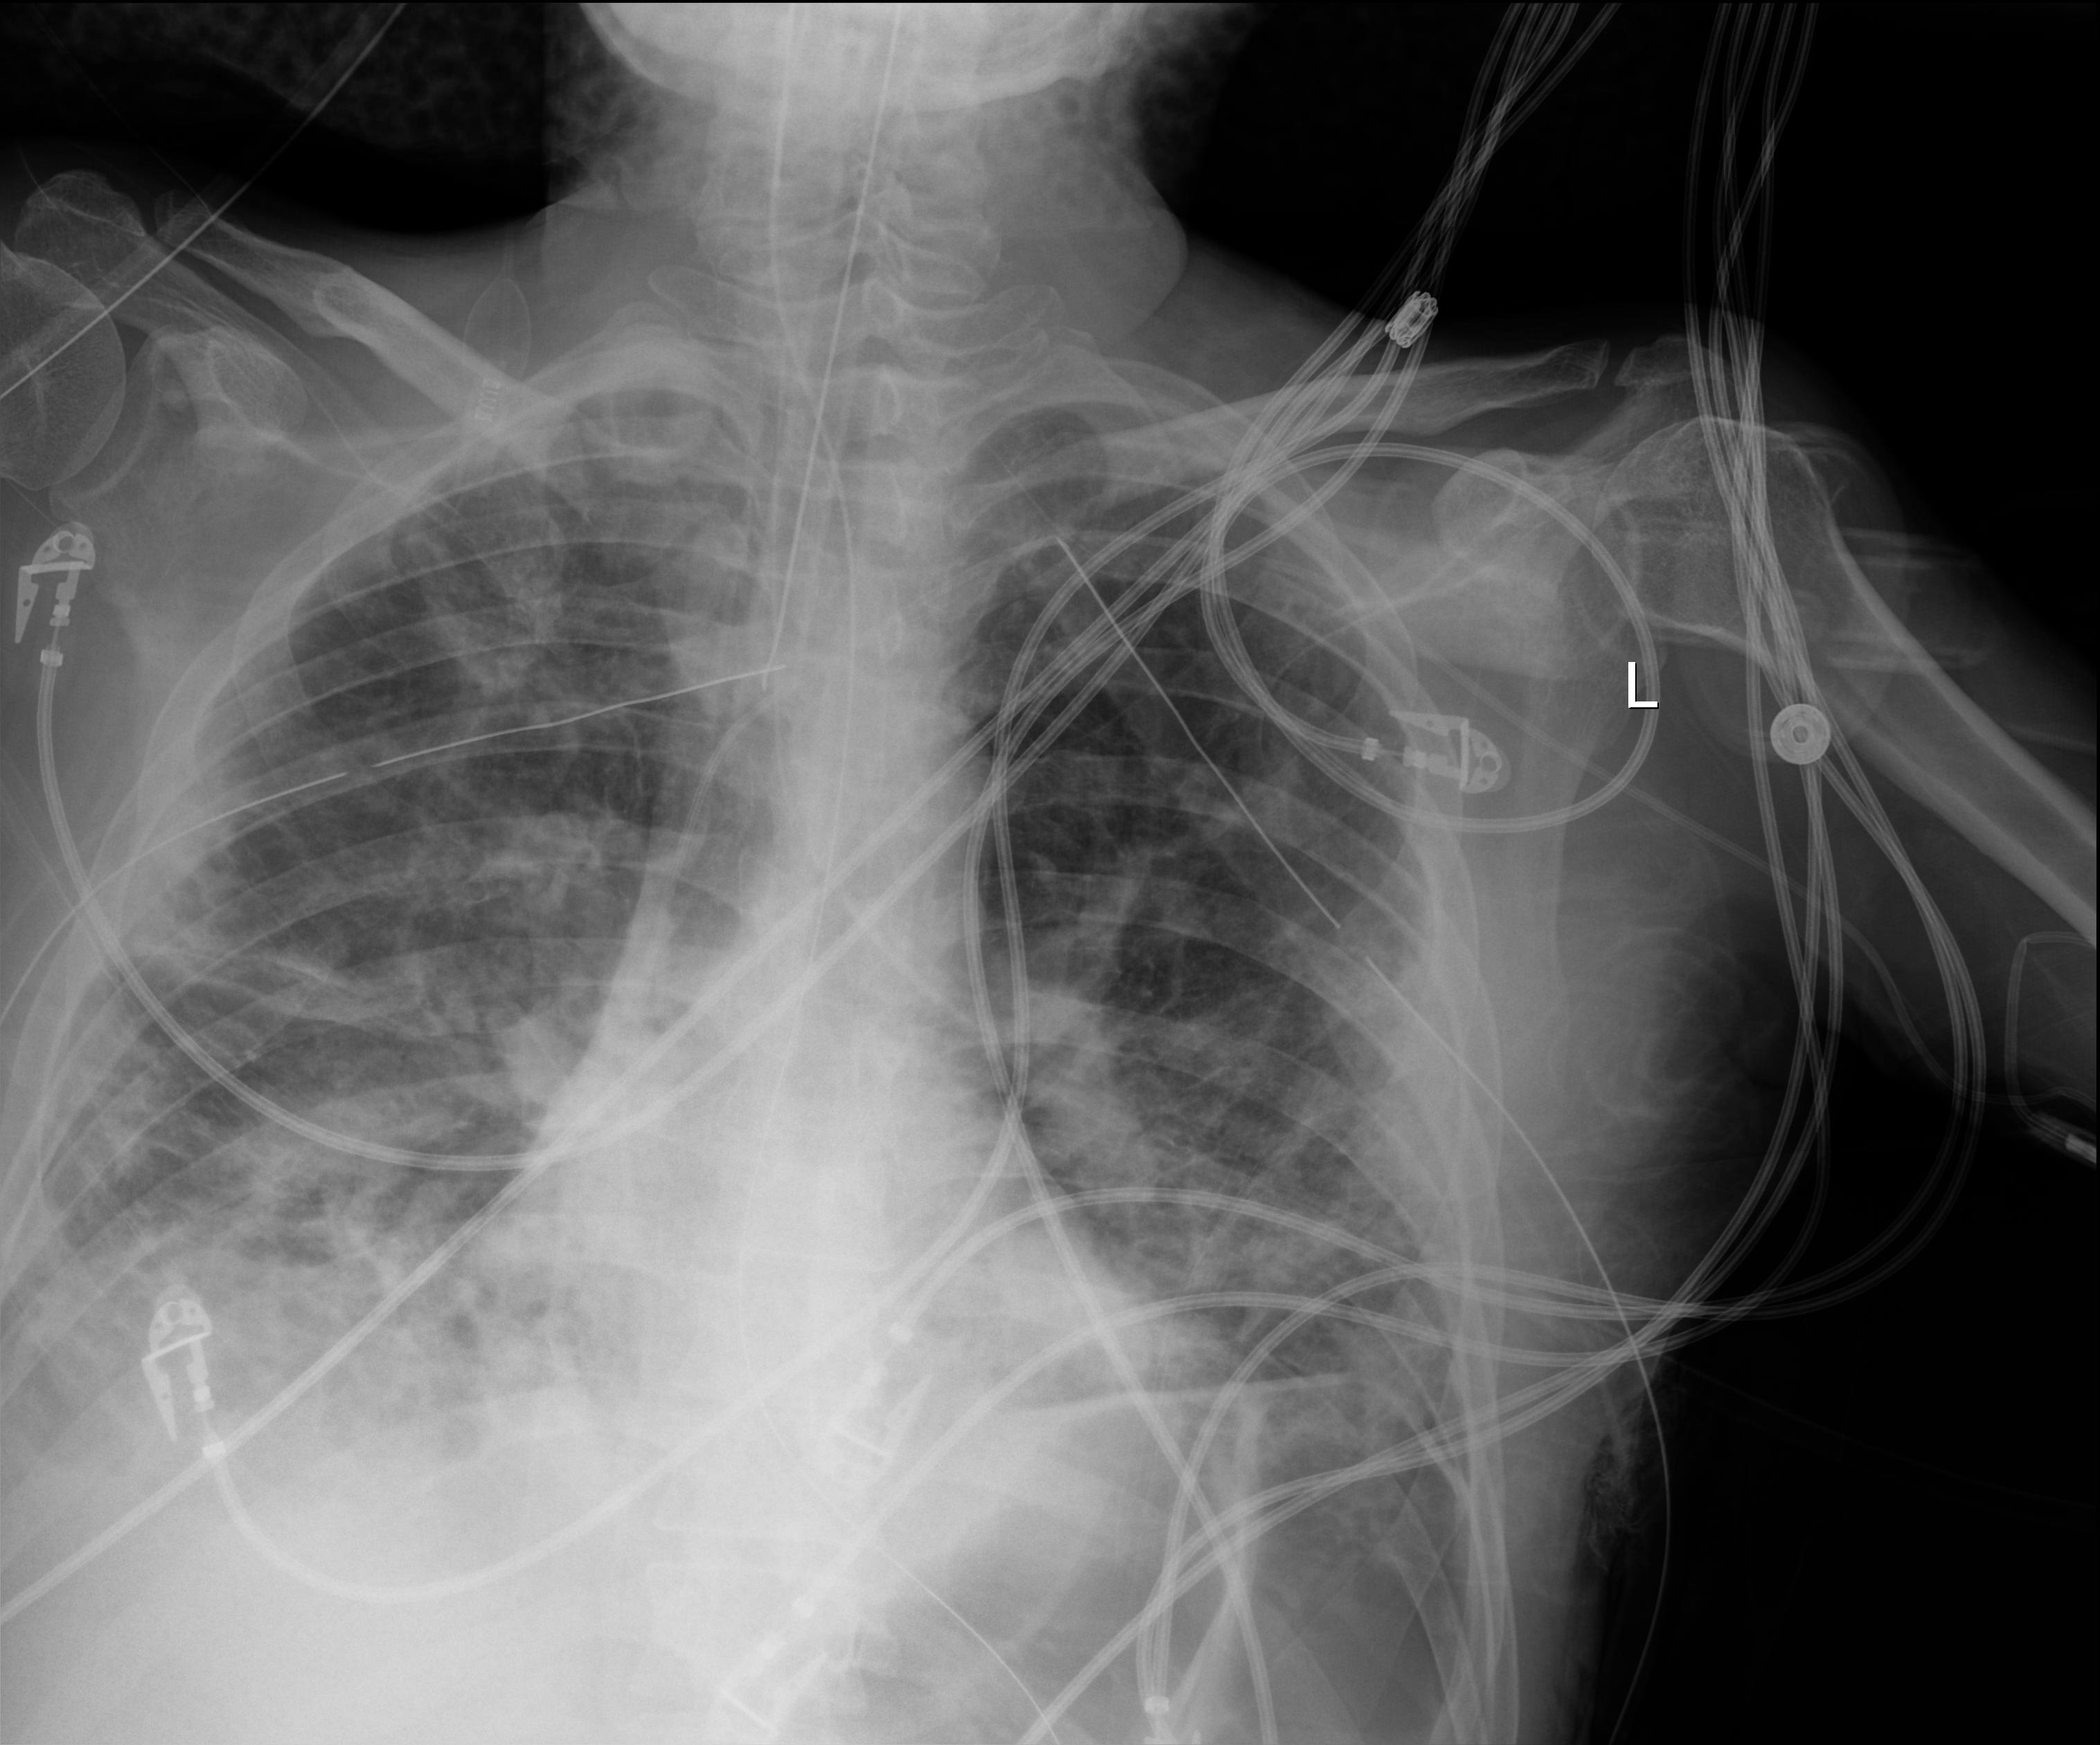
Chest X-ray (portable), anteroposterior (AP) projection. Male patient hospitalised with COVID-19, age 18–59 years.
Hospital-stay facts (about this admission, not read from this image; timing relative to this image not recorded):
- mechanically ventilated during this hospital stay: yes
- chronic kidney disease (admission record): no
- admitted to intensive care during this hospital stay: yes